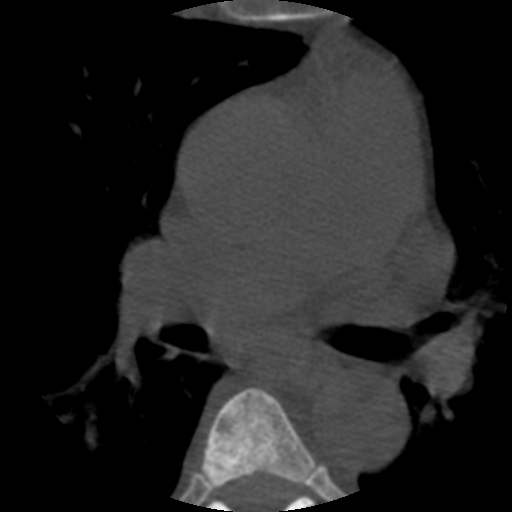
CT including the spine, one axial slice; reconstruction kernel STANDARD; bone window (W 1800 / L 400 HU); 1.25 mm slice thickness; 512 × 512 image matrix. Patient age 57 years. From the clinical record (not read from this slice): primary cancer: prostate.
Annotated regions visible in this slice (semi-automatic segmentation, software-assisted and operator-edited):
- T5 vertebra: box from (x=202, y=388) to (x=315, y=489) px
- T6 vertebra: (x=206, y=485)–(x=315, y=512)